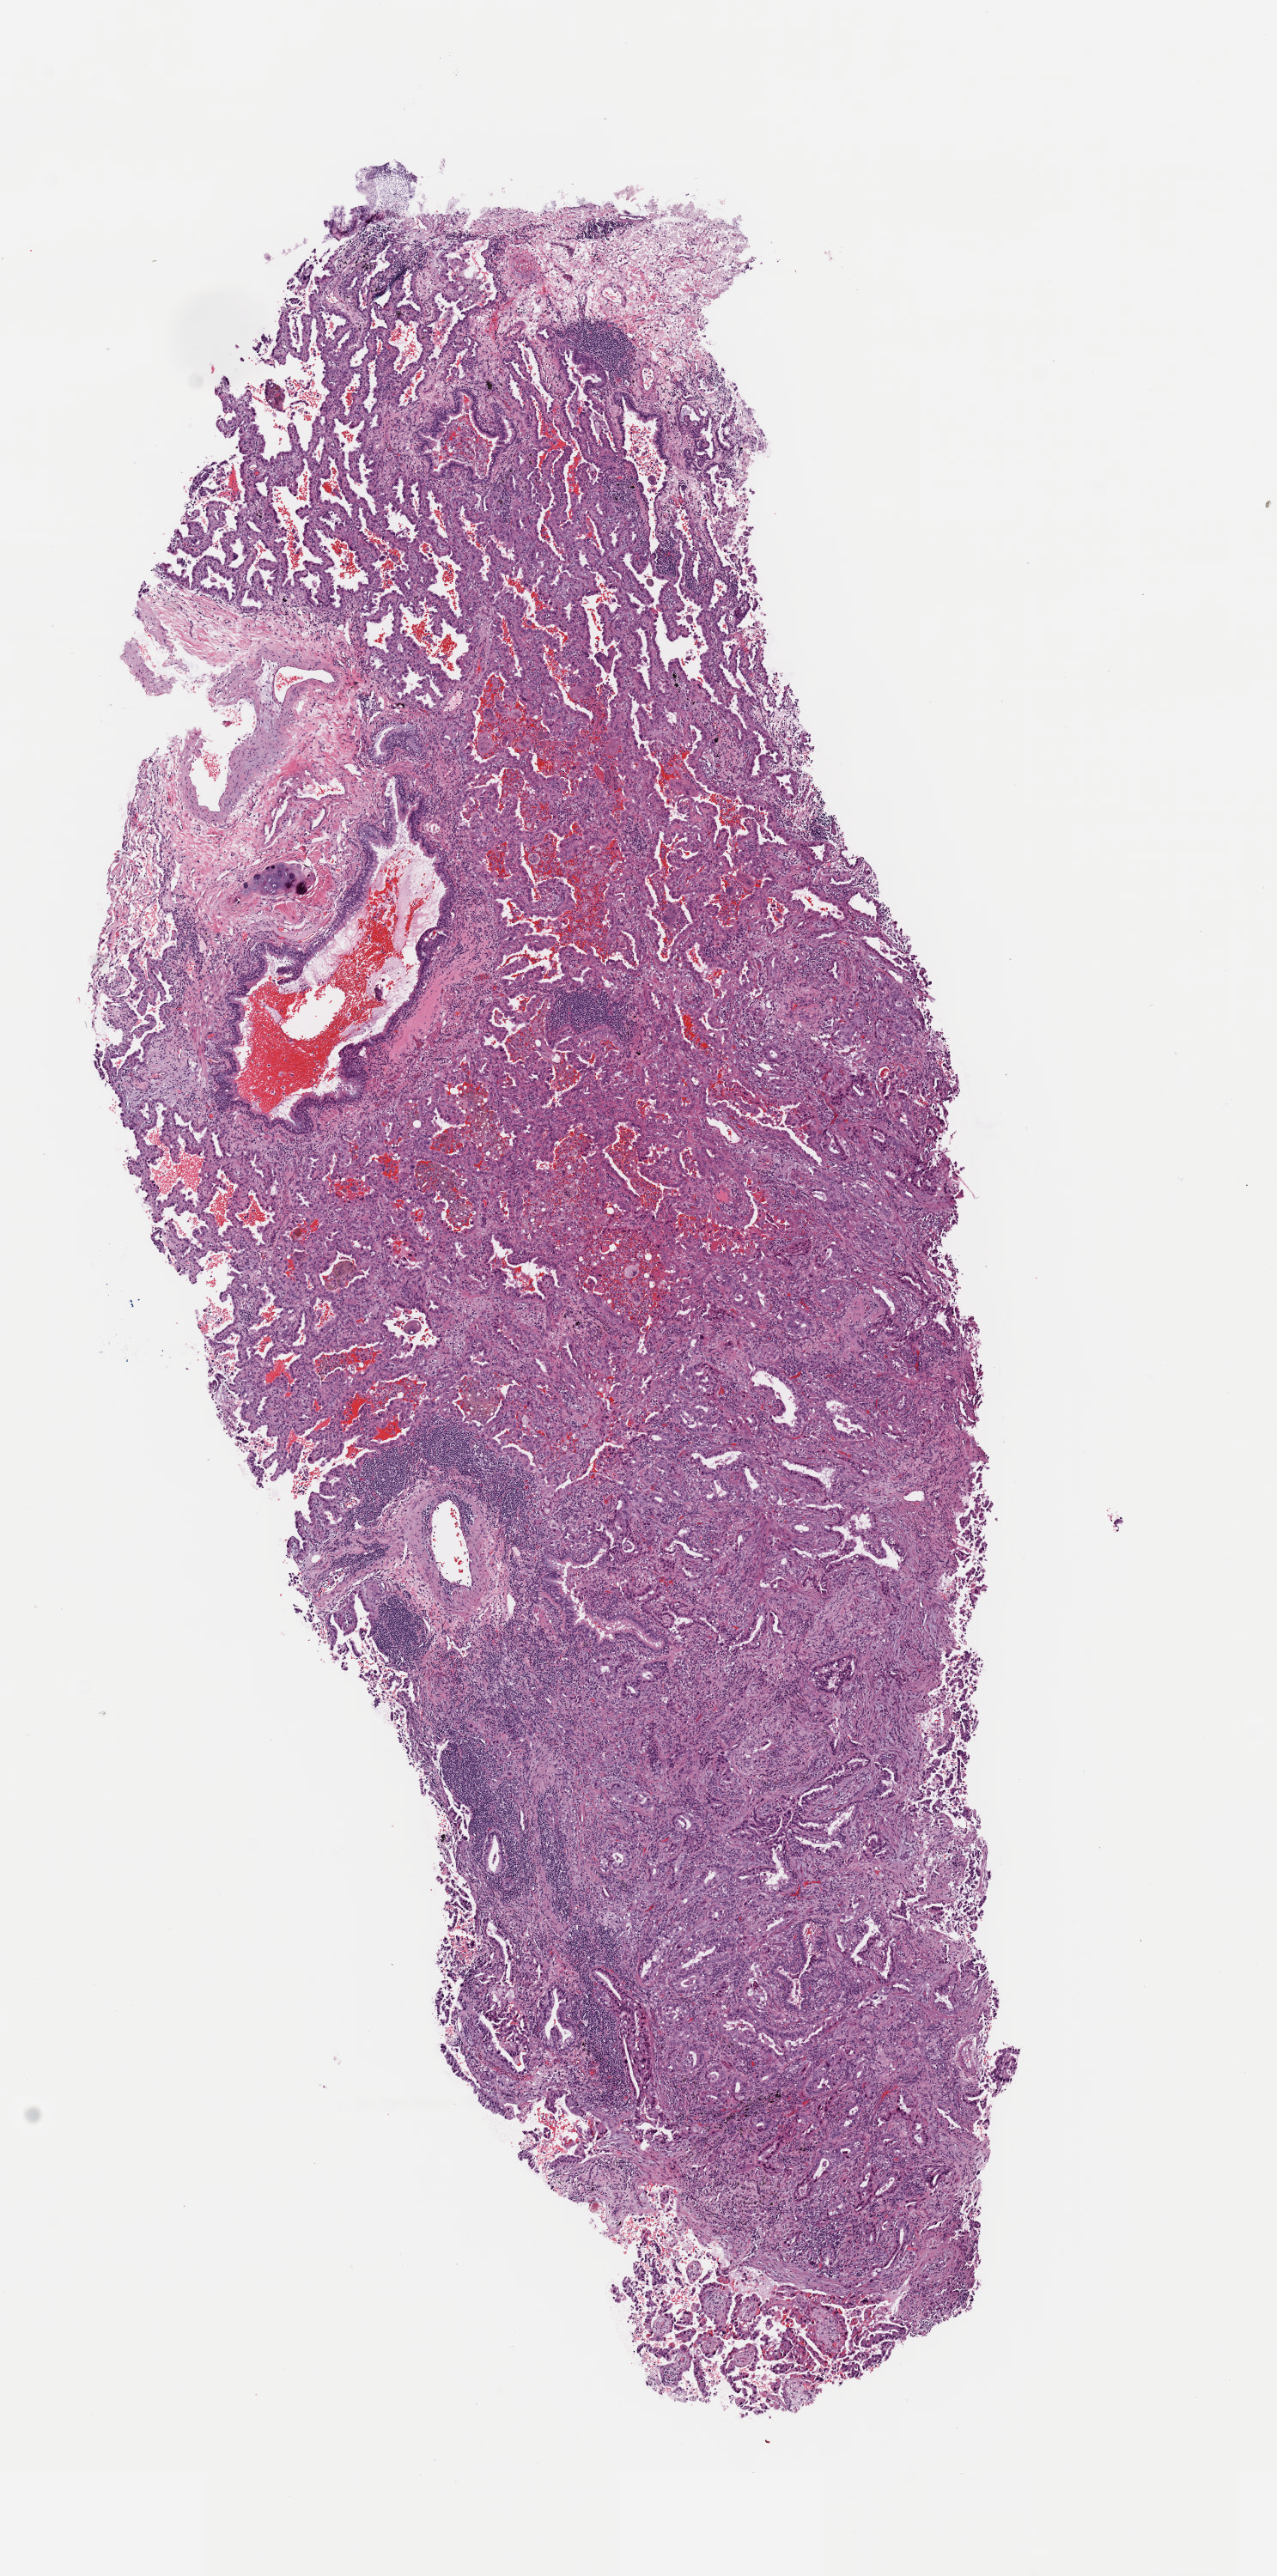
Whole-slide histology image, Hematoxylin and eosin (H&E) stained, low-resolution overview of the scanned area, about 5.9 x 11.9 mm (from a 40x scan), frozen section from the bottom of the tissue portion, primary tumour sample from the lung. Patient: female, age at initial diagnosis 72 years. Slide review estimates, as recorded: tumour cells 80%, tumour nuclei 80%, normal cells 5%, stromal cells 15%, necrosis 0%. Inflammatory infiltration, as recorded: lymphocyte infiltration 20%, monocyte infiltration 8%, neutrophil infiltration 0%.
Diagnosis: Adenocarcinoma, NOS (upper lobe, lung). AJCC pathologic stage: IB (7th edition).